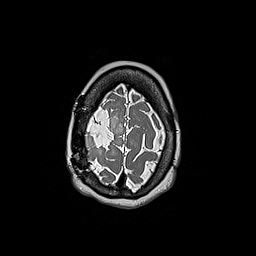
Brain MRI from a brain-tumour surgery series, one axial slice; slice 44 of 192 in the series (ordered by position); 1 mm slice thickness; 256 × 256 image matrix, field of view 250 × 250 mm. From the clinical record (not read from this slice): histopathology: Oligodendroglioma; WHO grade: 3; IDH mutation: yes; tumour location: Right Frontal.
Structures marked on this image (outlined manually by an expert reader):
- tumour: bounding box <85,136,98,149> (left, top, right, bottom; pixels)